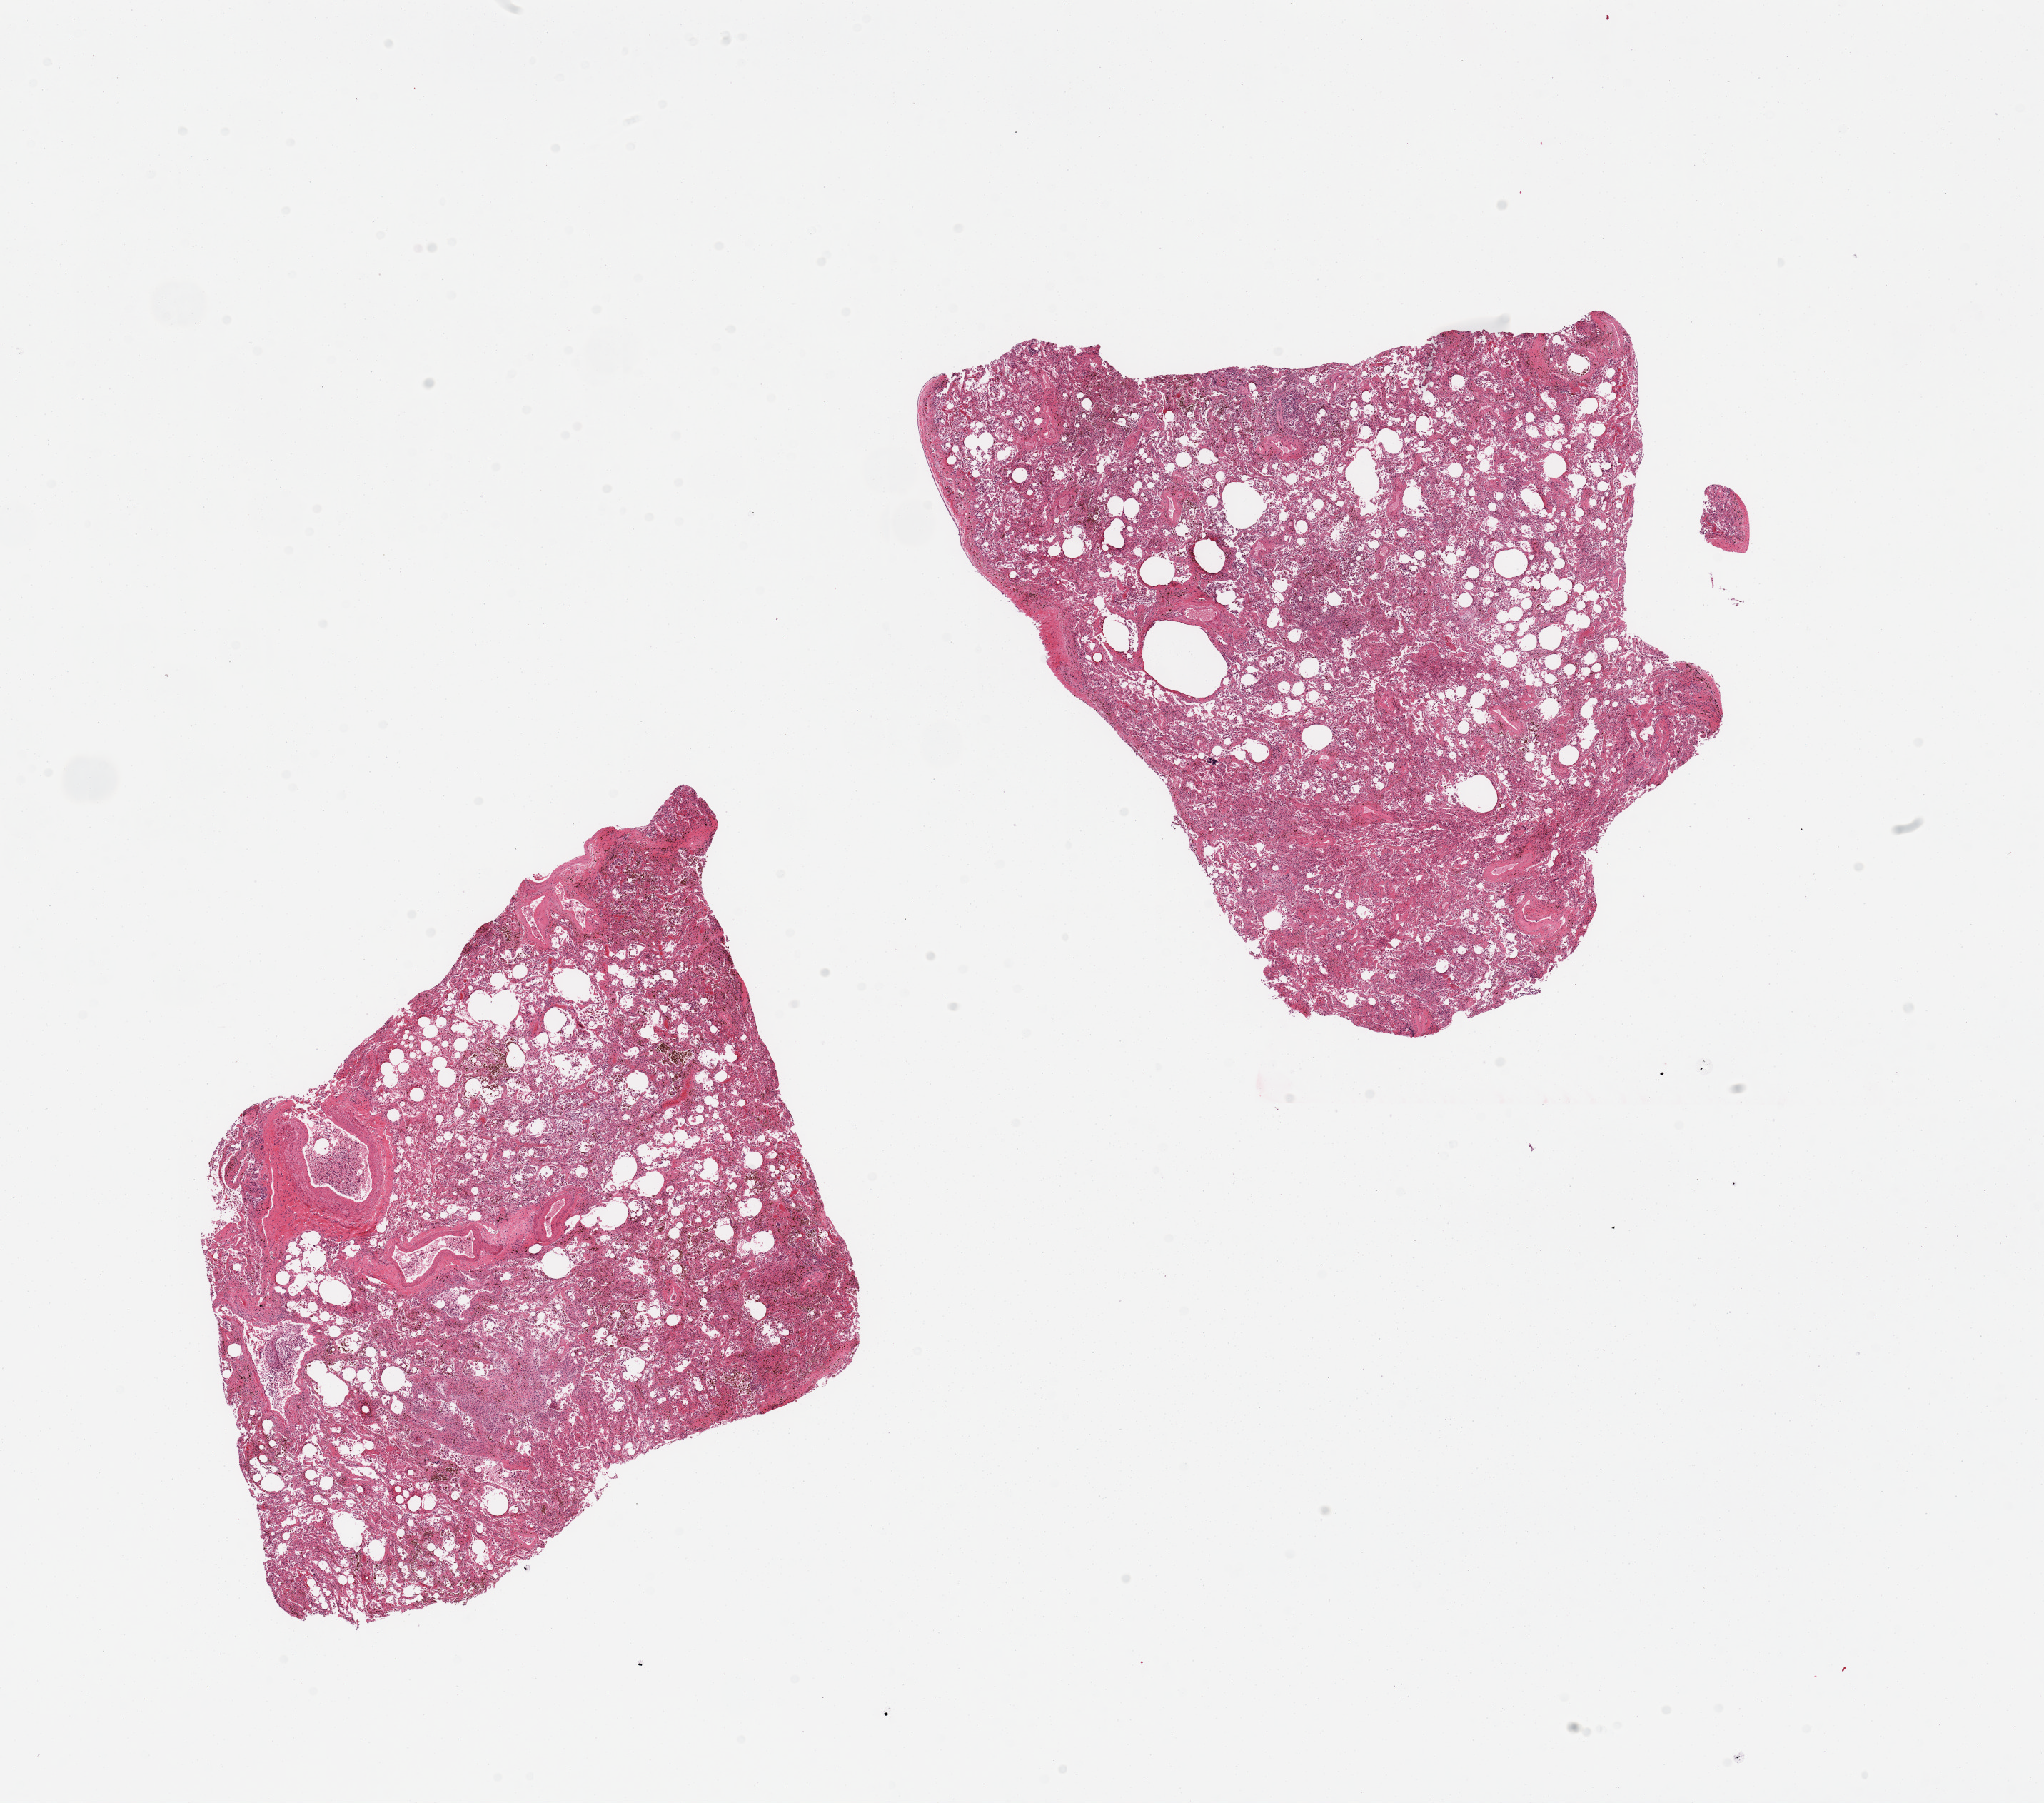
Digitized haematoxylin and eosin-stained section — low-resolution overview of the scanned area, about 22.6 x 20.0 mm (slide scanned at 20x), PAXgene-fixed paraffin-embedded (PFPE) section, target tissue: lung, donor tissue sample. Female donor.
Review note (as recorded): 2 pieces; pigmented alveolar macrophages & fibrosis.